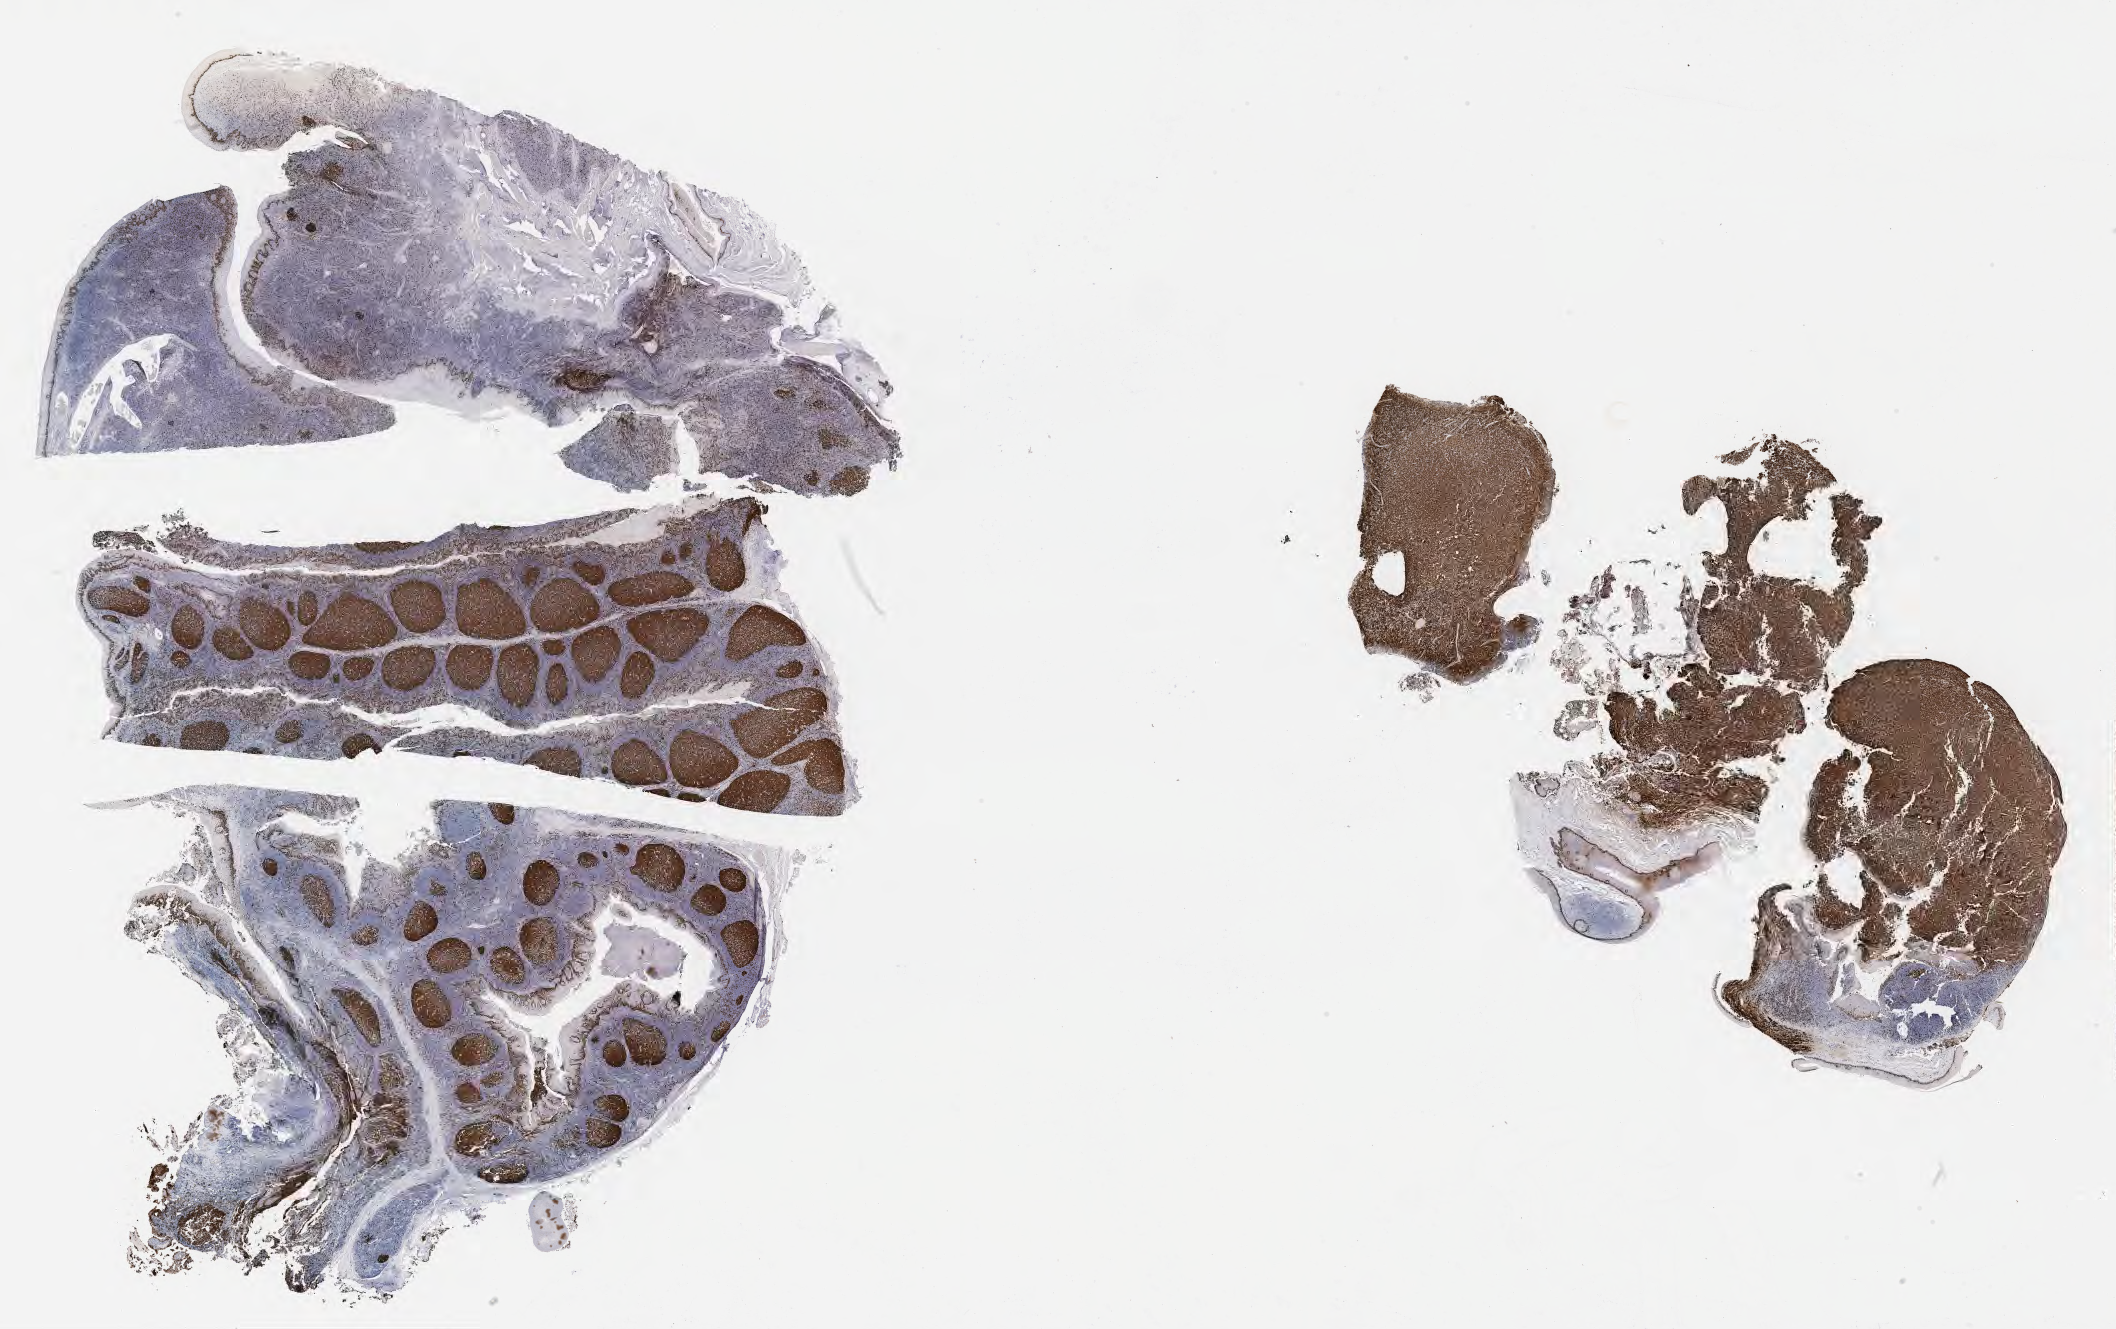
Immunohistochemistry (IHC) whole-slide image stained for Ki-67, shown as a low-resolution overview of the whole scanned area (about 34.2 x 21.5 mm). Specimen: tumor tissue. Male patient, age 63 years.
• histologic diagnosis: Burkitt lymphoma, NOS